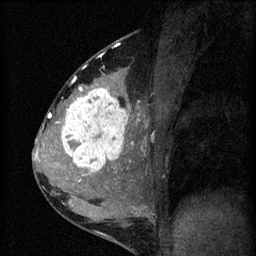
Breast MRI (dynamic contrast-enhanced), one sagittal slice; 3 images stored at this slice position (order not interpretable as contrast timing); 1.5 T; TE 4.2 ms, TR 8.2 ms; 2 mm slice thickness; 256 × 256 image matrix. Female patient, age 37 years.
Outlined on this slice (semi-automatic segmentation, software-assisted and operator-edited):
- analysis volume of interest (the breast-tissue region the enhancement analysis was run in; not a lesion): bounding box [x1, y1, x2, y2] px = [53, 78, 140, 181]
- tumour enhancement mask (voxels above the 70 % enhancement threshold inside the analysis volume of interest): [57, 88, 140, 181]